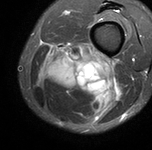
MRI of an extremity soft-tissue mass, one axial slice. Slice 26 of 90 in the series (ordered by position). STIR. MR volume resampled by the dataset authors to the PET/CT grid (not the native acquisition matrix). 3.27 mm slice thickness. 152 × 150 image matrix, field of view 148 × 146 mm. Male patient. From the clinical record (not read from this slice): histological type: undifferentiated pleomorphic liposarcoma; grade: high; site of the primary tumour: left thigh.
Annotated regions visible in this slice (expert contour drawn on MRI and transferred to this co-registered scan by the dataset authors):
- gross tumour volume including surrounding oedema: bounding box (x1, y1, x2, y2) in pixels: (39, 43, 124, 117)